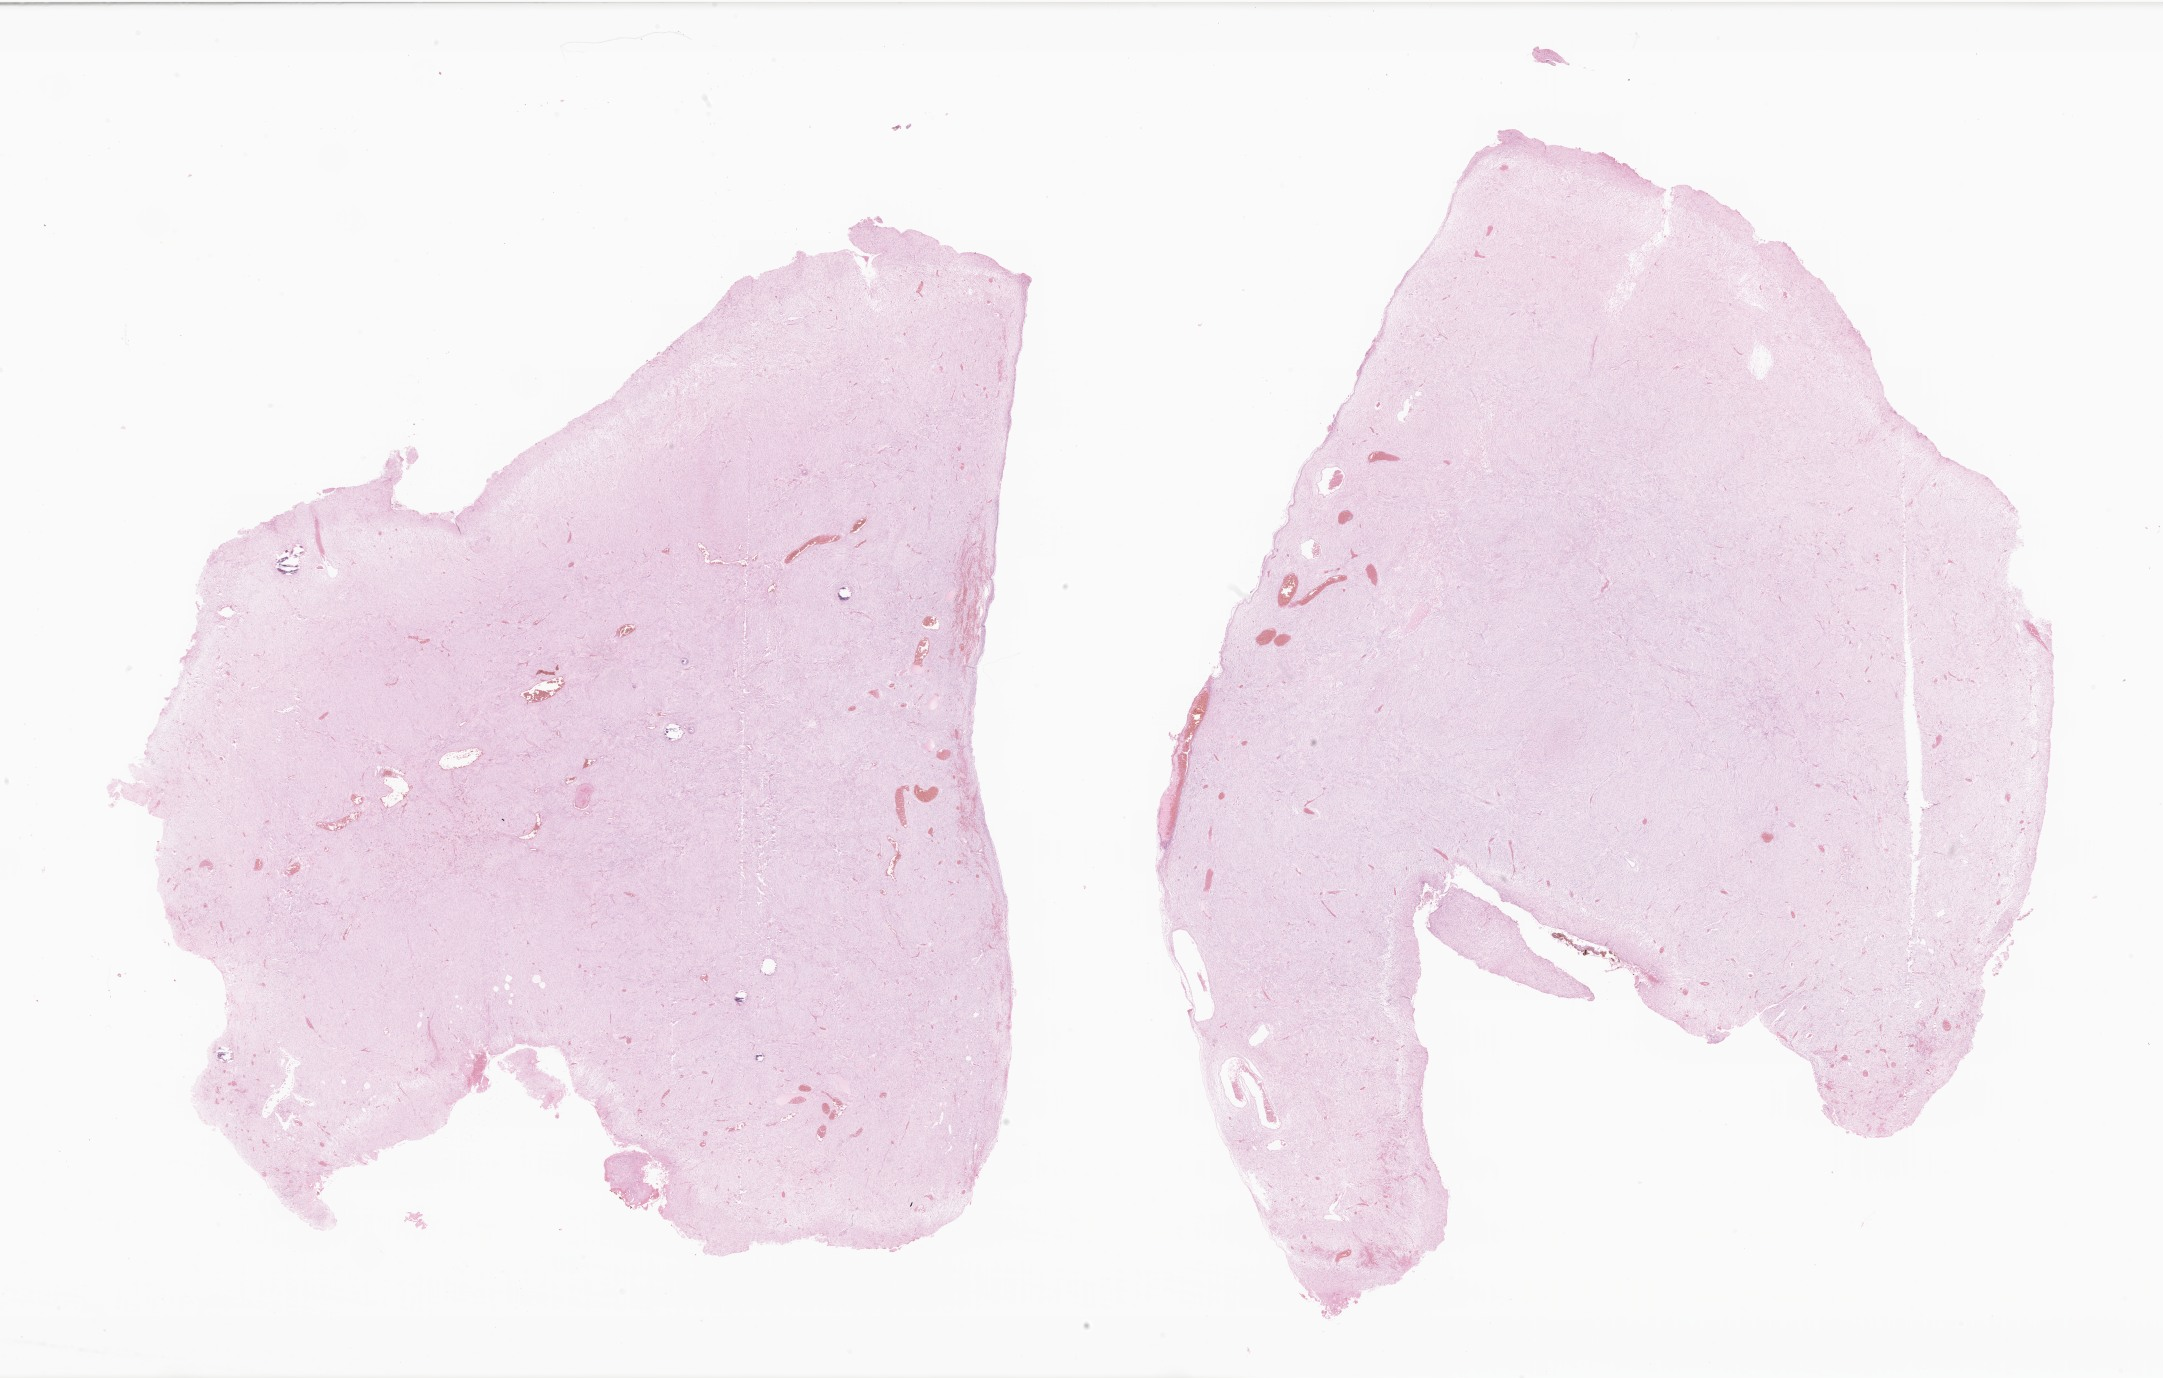
Whole-slide image, H&E stain of tumor tissue from the cerebral ventricle, a low-resolution overview of the entire scanned area, about 36.5 x 23.2 mm, FFPE section. Patient female; age 125 months (10 years 5 months).
• diagnosis: Meningioma, NOS